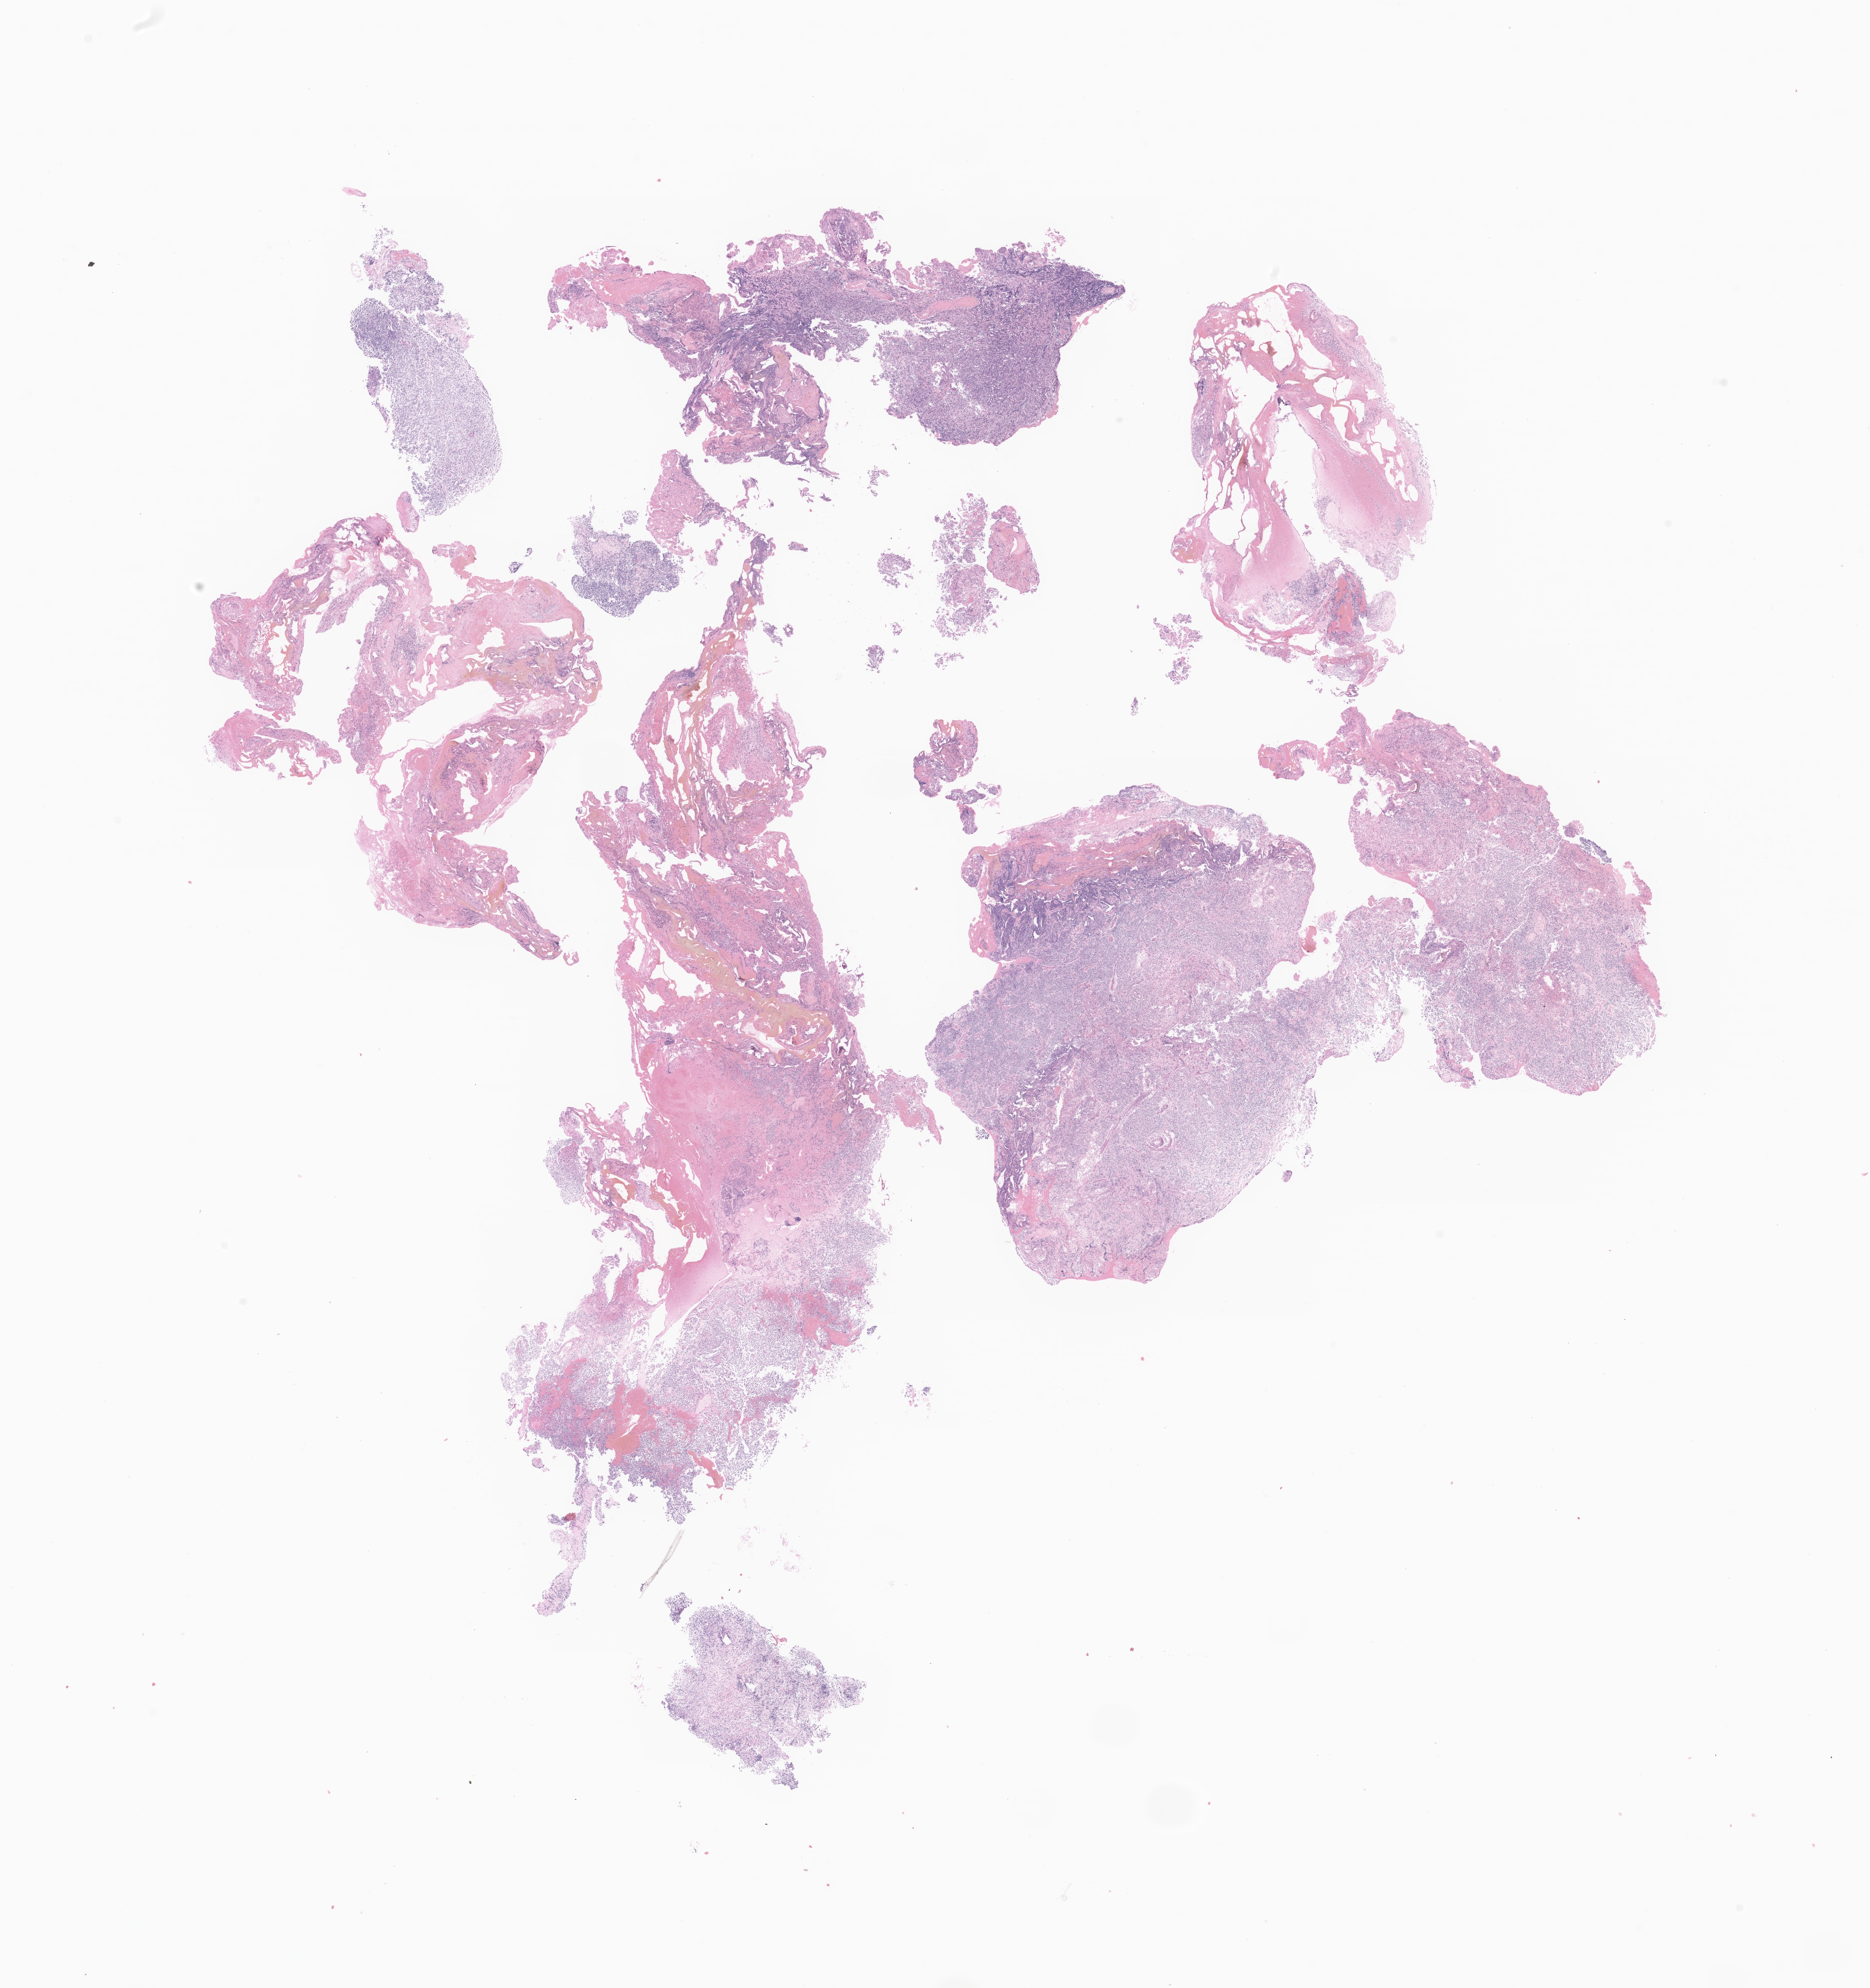
Digitized haematoxylin and eosin-stained section of tumor tissue from the brain — whole scanned area (about 17.8 x 18.9 mm) shown as a low-resolution overview, formalin-fixed, paraffin-embedded (FFPE) tissue. Patient: male, age 144 months (12 years).
* diagnosis (ICD-O-3 morphology term): Medulloblastoma, NOS